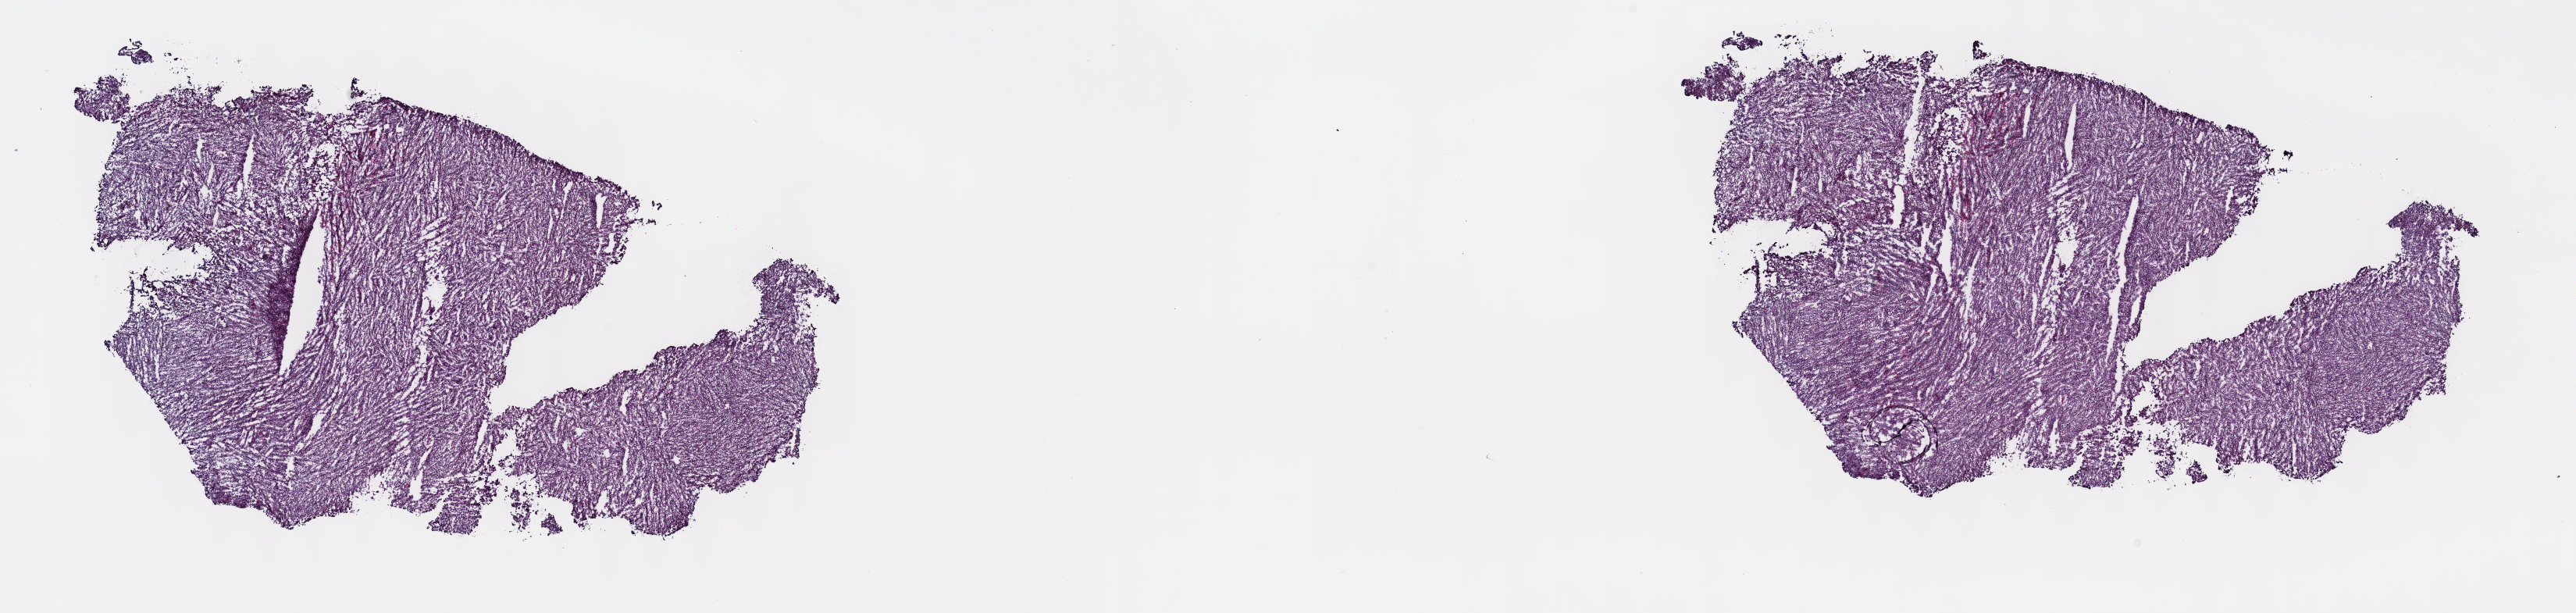
H&E-stained whole-slide image, low-resolution overview of the scanned area, about 26.7 x 6.3 mm (from a 40x scan); frozen section from the top of the tissue portion; metastatic tumour sample, sampled site not recorded. Female, age 63 years at initial diagnosis. Pathologist review of this section (percent, as recorded): tumour cells 90%, tumour nuclei 95%, normal cells 0%, stromal cells 5%, necrosis 5%. Inflammatory infiltration, as recorded: lymphocyte infiltration 0%, monocyte infiltration 0%, neutrophil infiltration 0%.
This section: metastatic tumour tissue. Patient diagnosis: Malignant melanoma, NOS.